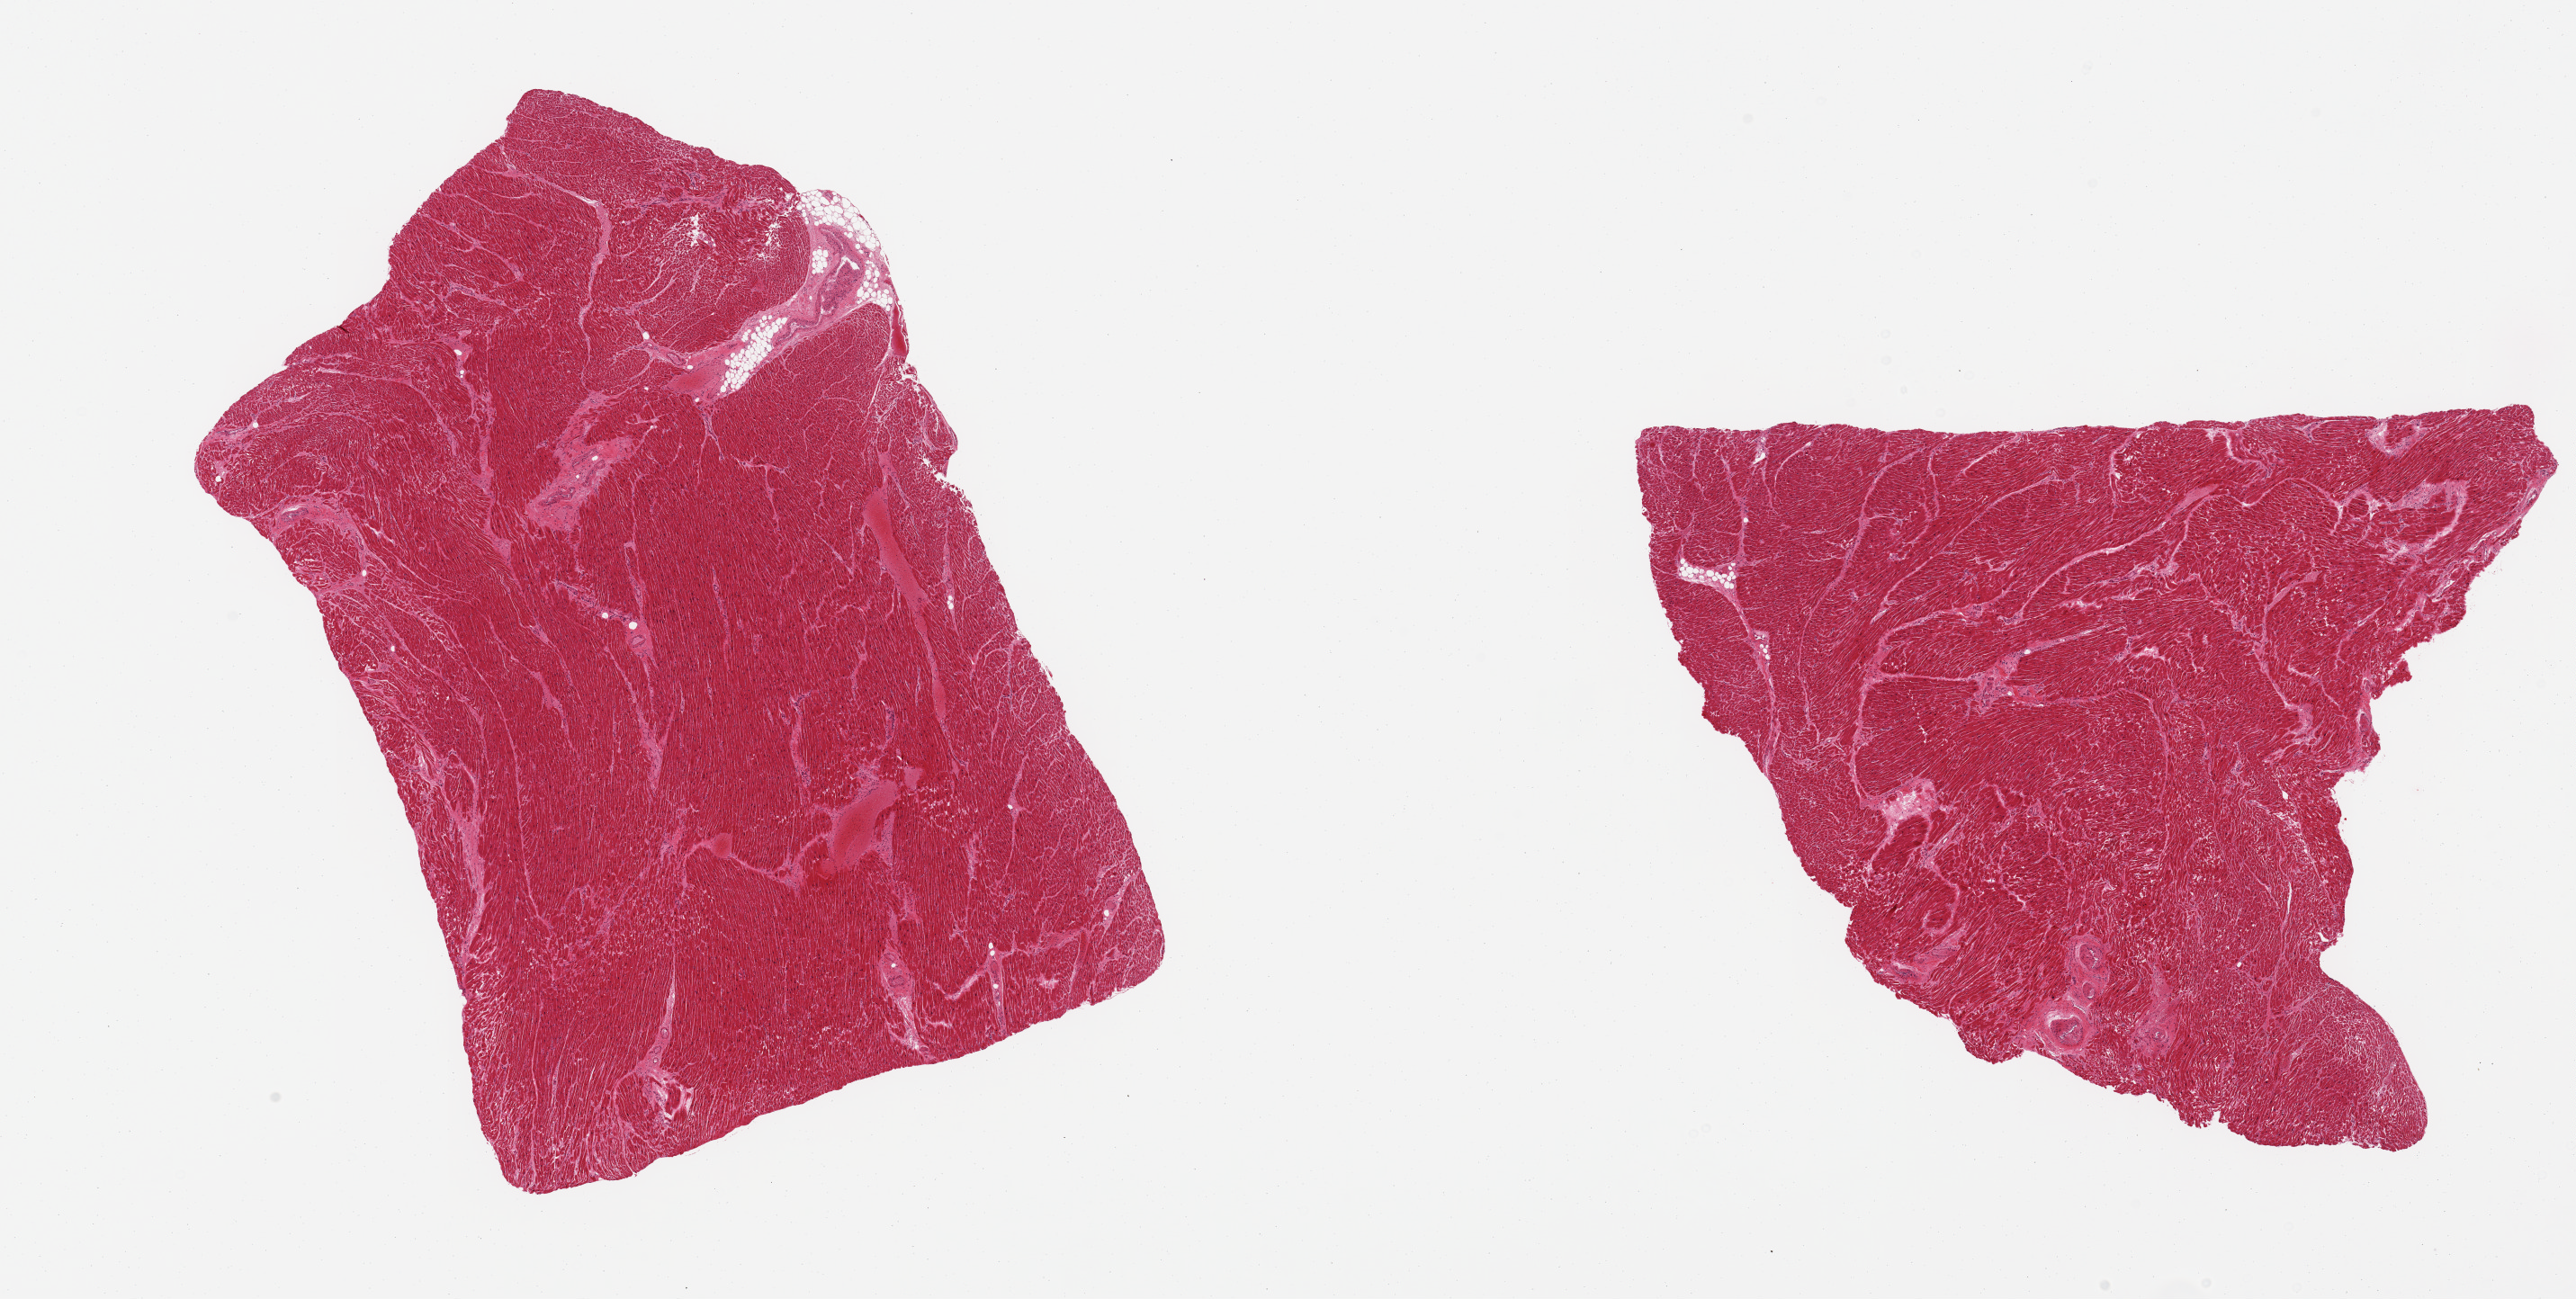
H&E whole-slide image, shown as a low-resolution overview of the whole scanned area (about 22.6 x 11.4 mm), PAXgene-fixed paraffin-embedded (PFPE) section, sampled site (target tissue): heart, tissue donor sample. Donor sex: male.
Reviewer comment on this tissue sample: 2 pieces, minimal interstitial fibrosis/chronic ischemic changes.